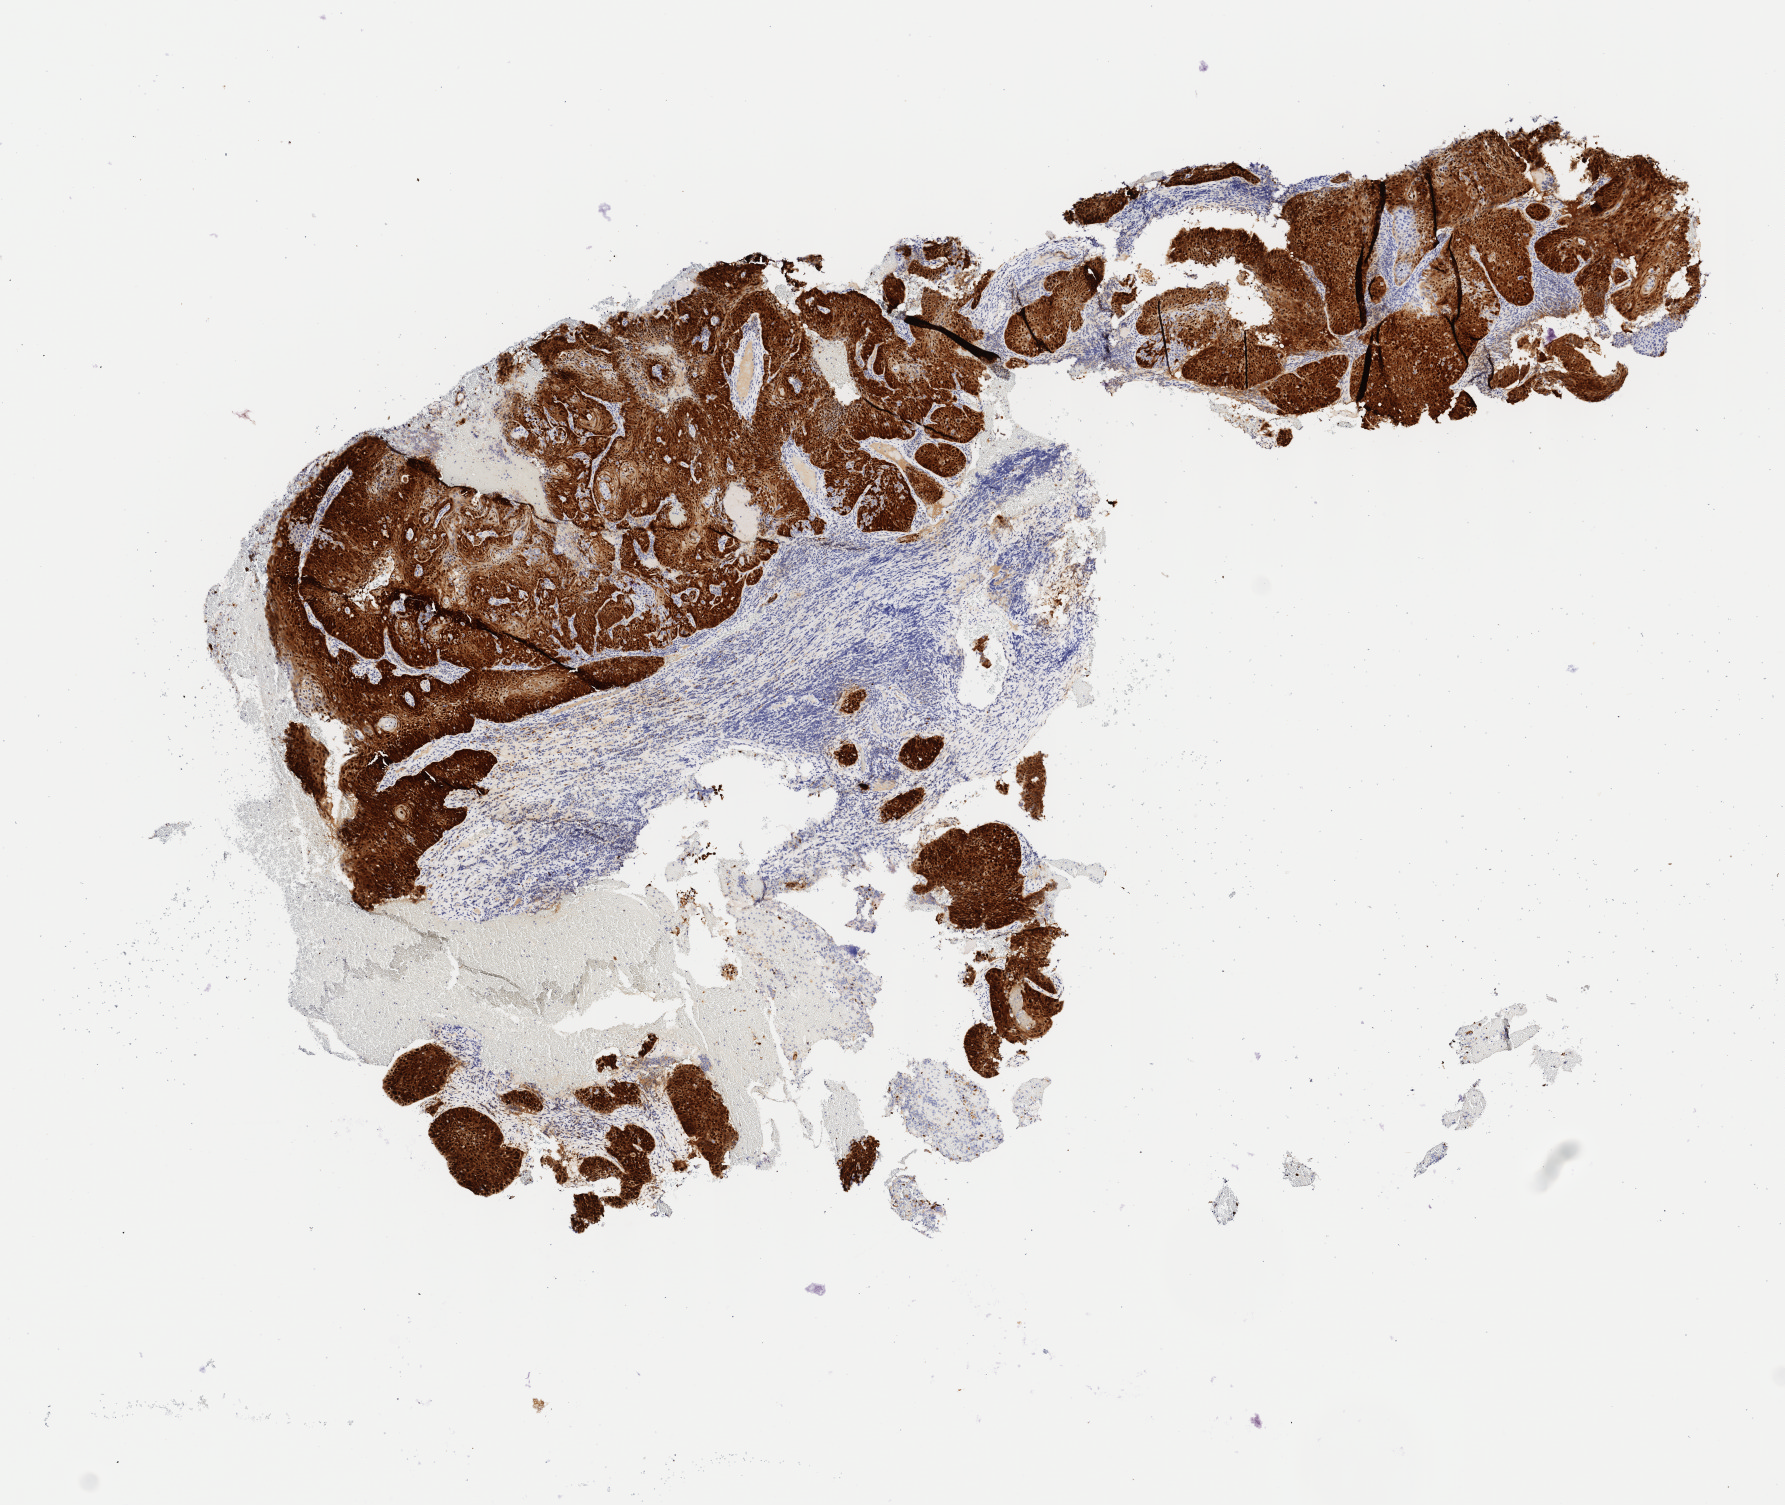
IHC for p16 (p16INK4a), whole-slide image — low-resolution overview of the scanned area, about 7.1 x 6.0 mm. Specimen: tumor tissue. Site: cervix. Patient female; 65 years old.
• histologic diagnosis: Squamous cell carcinoma, keratinizing, NOS